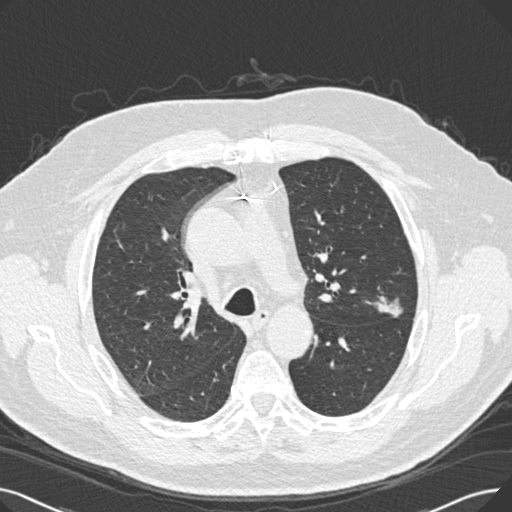
Low-dose screening chest CT, one axial slice; slice 176 of 269 in the series (ordered by position); reconstruction kernel B30f; 120 kVp; lung window (W 1500 / L -600 HU); 1 mm slice thickness; 512 × 512 image matrix.
Annotated regions visible in this slice (outlined manually by an expert reader):
- lesion 1 (tumor, upper lobe of left lung): bounding box (x1, y1, x2, y2) in pixels: (371, 292, 403, 318)